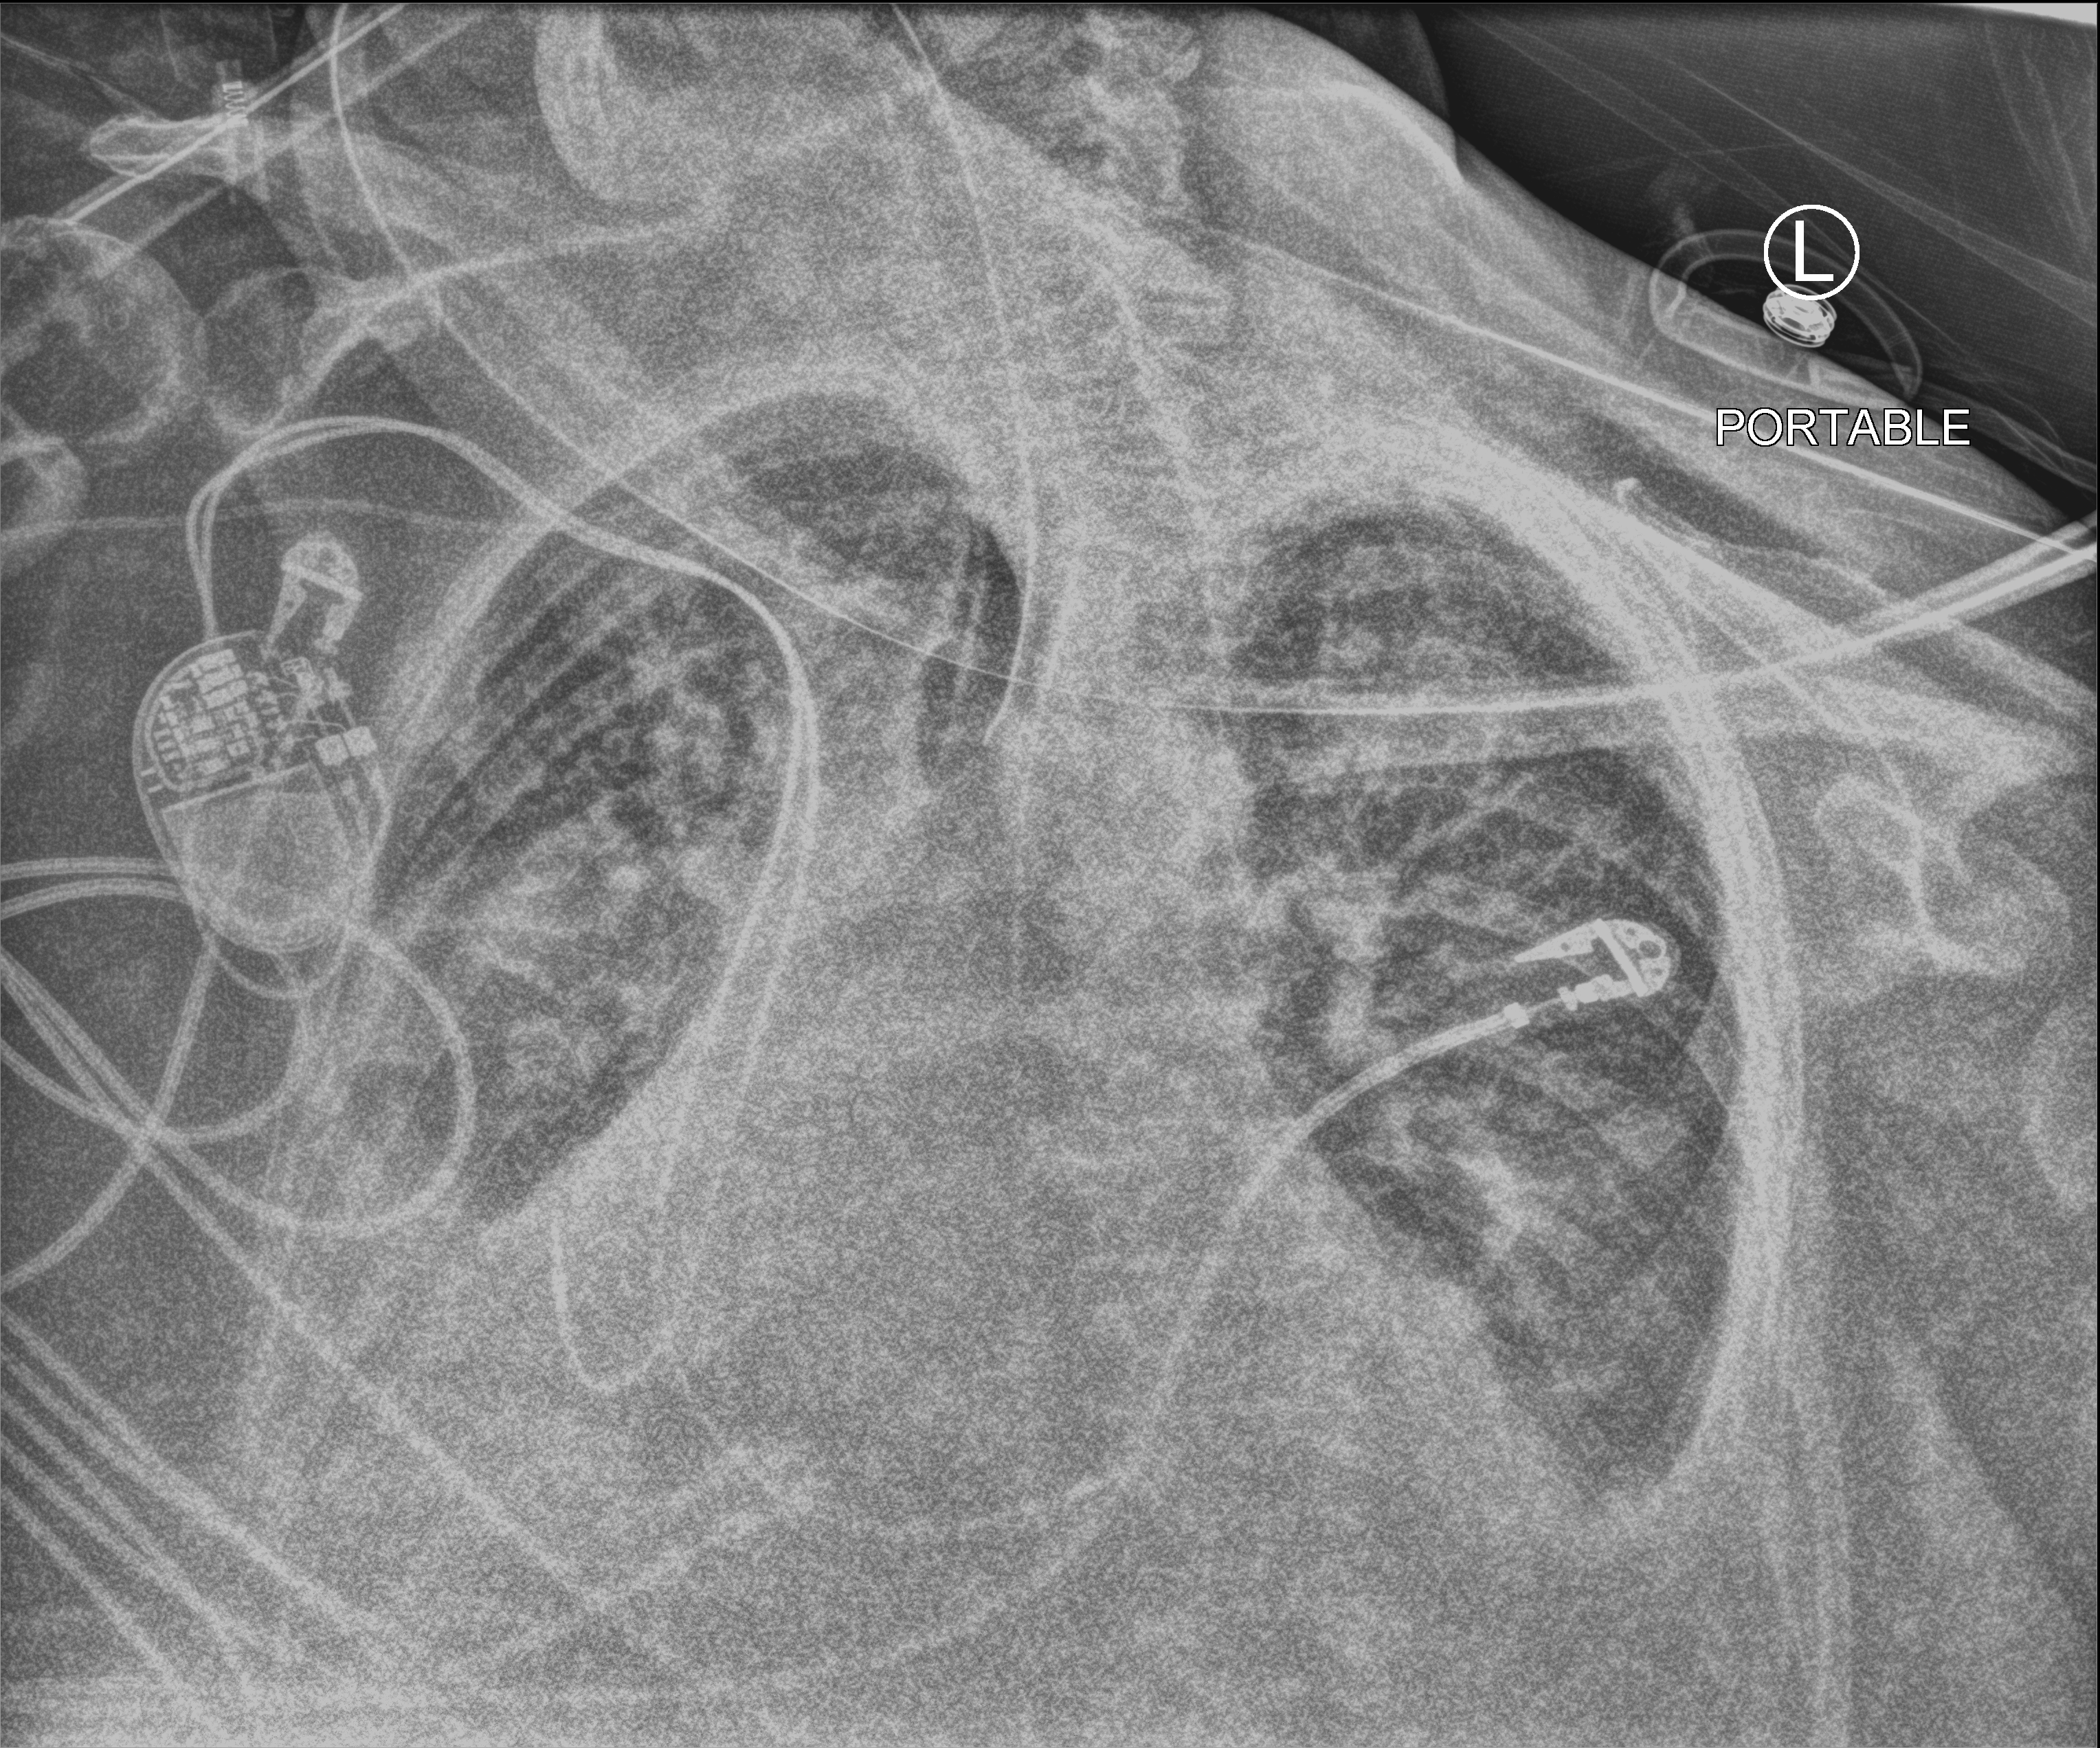
Chest X-ray (portable); anteroposterior (AP) projection. Female patient hospitalised with COVID-19, age 75–90 years.
From the hospital-stay record, not from the radiograph (when in the stay this image was taken is not recorded):
- mechanically ventilated during this hospital stay: yes